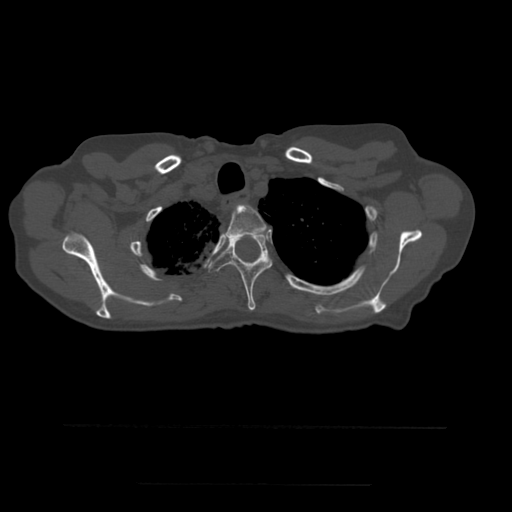
CT including the spine, one axial slice. Position 424 of 544 along the scan axis. Bone window (W 1800 / L 400 HU). 1.25 mm slice thickness. 512 × 512 image matrix, field of view 350 × 350 mm. Patient age 58 years. Case-level facts recorded for this patient, not image findings: primary cancer: lung.
Outlined on this slice (semi-automatic segmentation, software-assisted and operator-edited):
- T2 vertebra: bounding box <224,205,267,238> (left, top, right, bottom; pixels)
- T3 vertebra: <209,234,273,311>